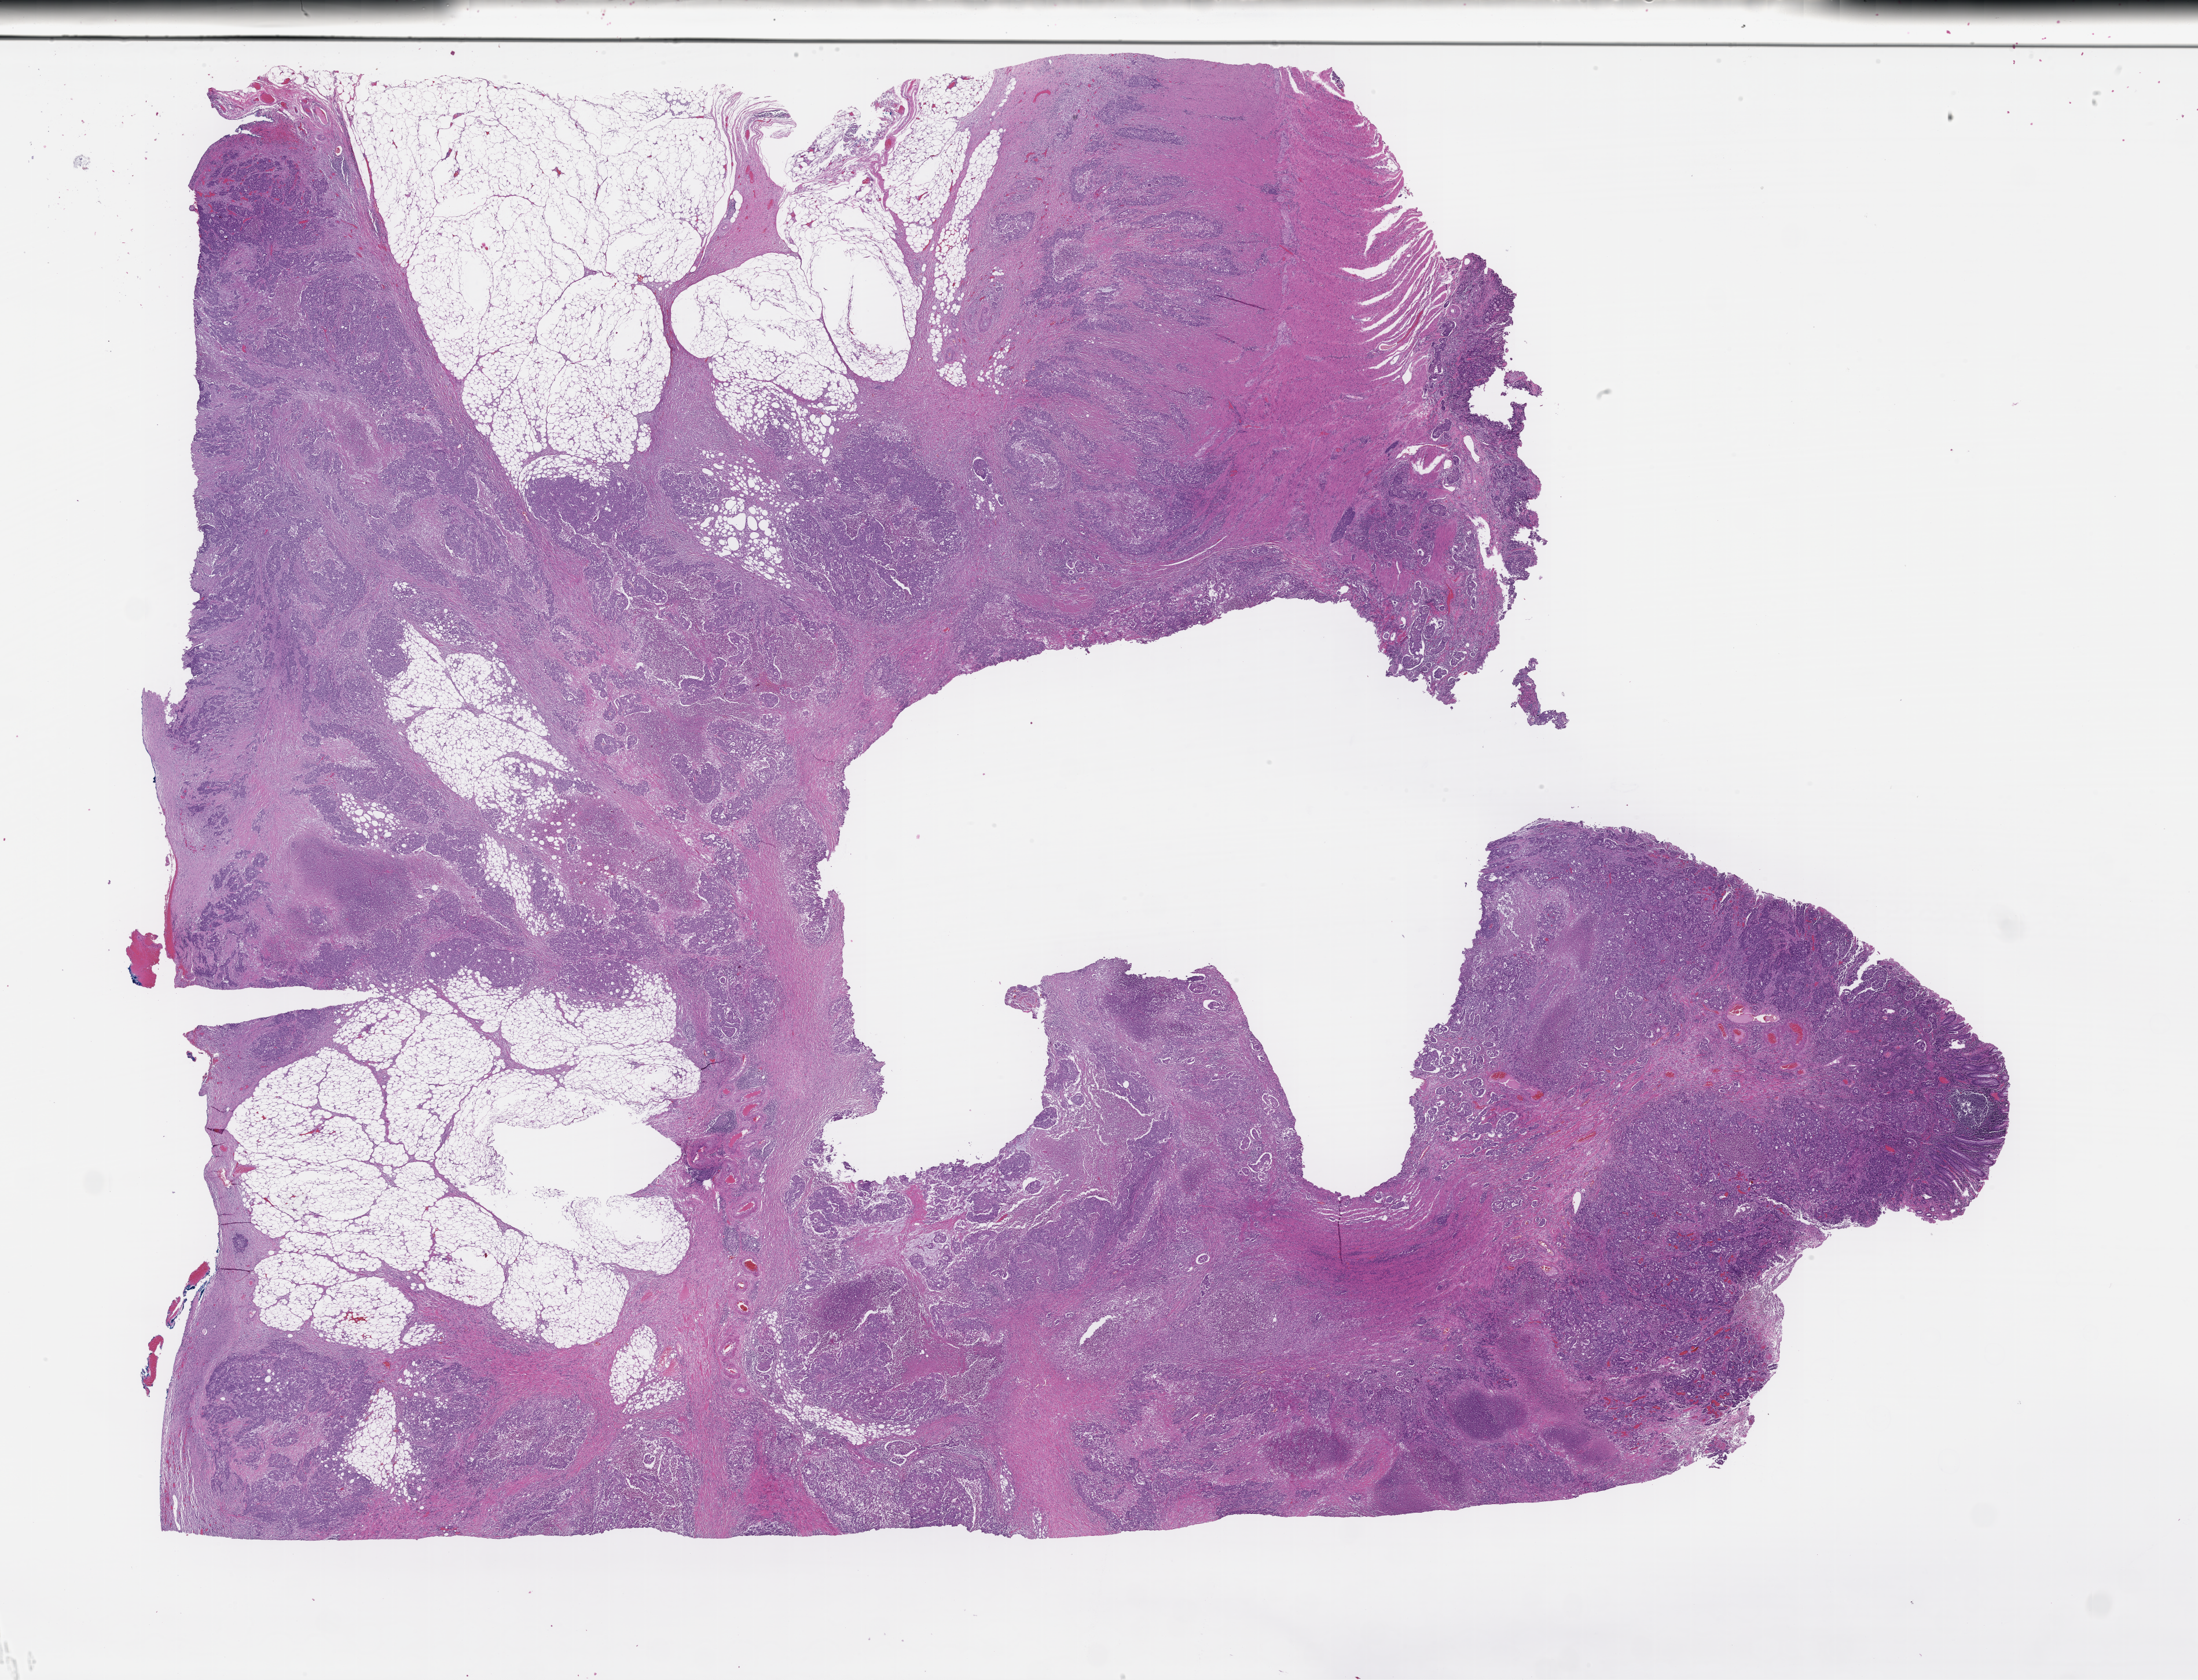
Whole-slide image, H&E stain — a low-resolution overview of the entire scanned area, about 30.7 x 23.4 mm; formalin-fixed paraffin-embedded section; tissue site: colon; specimen time point: archival tissue. Female patient.
* this section: primary tumor
* diagnosis: Colorectal Carcinoma